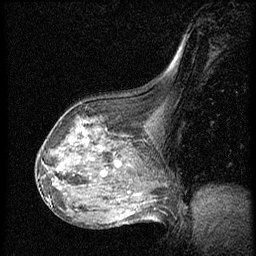
Breast MRI (dynamic contrast-enhanced), one sagittal slice; slice 37 of 56 in the series (ordered by position); dynamic contrast-enhanced series, image 2 of 3 at this slice position (ordered by acquisition); 1.5 T; TE 4.2 ms, TR 20.4 ms; 256 × 256 image matrix, field of view 200 × 200 mm. Female patient, age 64 years. From the clinical record (not read from this slice): setting: breast cancer imaged before/during neoadjuvant chemotherapy; receptor status: HR-positive, HER2-negative.
Annotated regions visible in this slice (semi-automatic segmentation, software-assisted and operator-edited):
- analysis volume of interest (the breast-tissue region the enhancement analysis was run in; not a lesion): bounding box (x1, y1, x2, y2) in pixels: (48, 101, 142, 186)
- tumour enhancement mask (voxels above the 70 % enhancement threshold inside the analysis volume of interest): (85, 142, 87, 144)